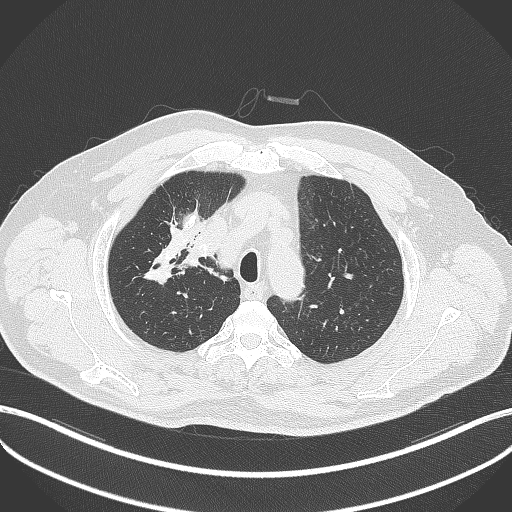
Chest CT, one axial slice. Position 312 of 411 along the scan axis. Reconstruction kernel B70f. Lung window (W 1500 / L -600 HU). 1 mm slice thickness. 512 × 512 image matrix. Male patient, age 60 years. From the clinical record (not read from this slice): clinical TNM (as recorded): T1b N1 M0.
Structures marked on this image (rectangle marked by the reading radiologist):
- lung tumour (recorded histology: squamous cell carcinoma): box from (x=184, y=241) to (x=204, y=272) px